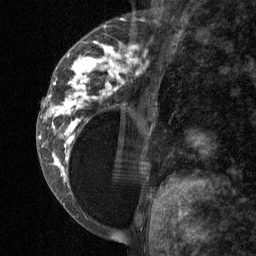
Breast MRI (dynamic contrast-enhanced), one sagittal slice. Slice 23 of 64 in the series (ordered by position). Dynamic contrast-enhanced study with each time point stored as its own series, time point 2 of 3 at this slice position (early post-contrast, ordered by acquisition time). 1.5 T. TE 4.8 ms, TR 27 ms. 256 × 256 image matrix. Patient: female, 34 years. Case-level facts recorded for this patient, not image findings: setting: breast cancer imaged before/during neoadjuvant chemotherapy; receptor status: HR-positive, HER2-negative.
Annotated regions visible in this slice (semi-automatically segmented with operator editing):
- analysis volume of interest (the breast-tissue region the enhancement analysis was run in; not a lesion): bounding box [x1, y1, x2, y2] px = [41, 23, 157, 197]
- tumour enhancement mask (voxels above the 90 % enhancement threshold inside the analysis volume of interest): [42, 42, 146, 180]